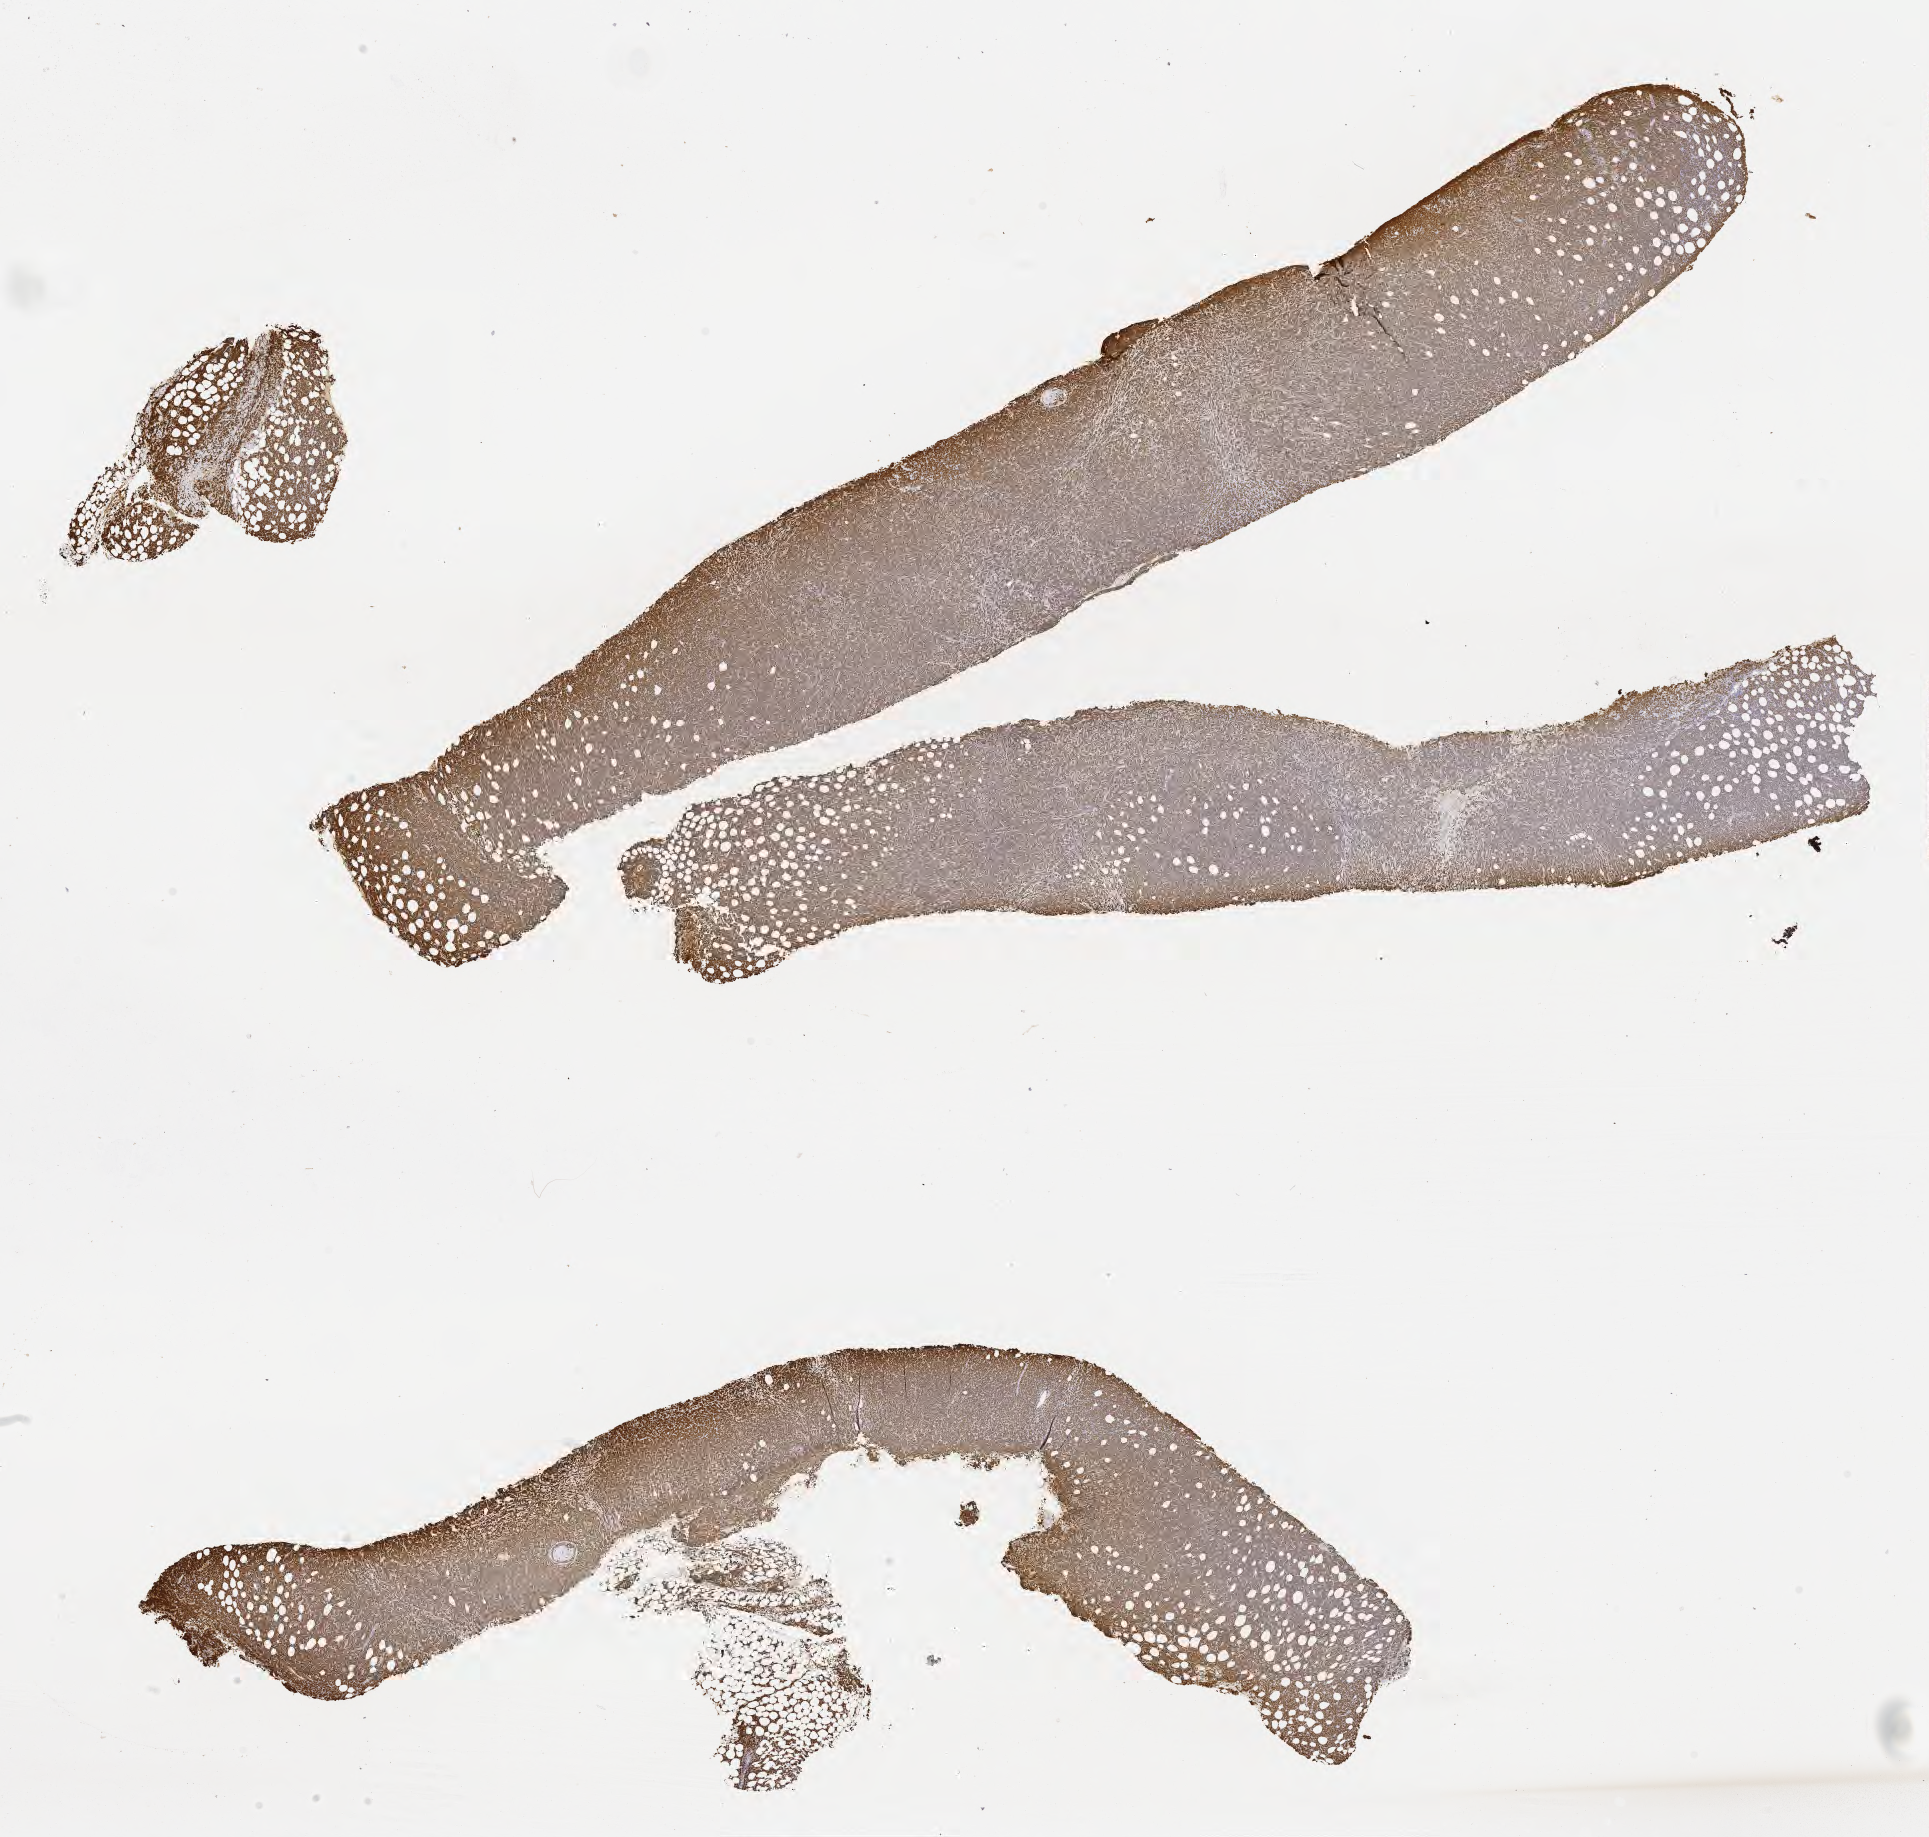
Whole-slide image, immunohistochemical stain for Ki-67 — a low-resolution overview of the entire scanned area, about 15.6 x 14.9 mm; tumor tissue. Patient female; aged 43.
- histologic diagnosis: Burkitt lymphoma, NOS